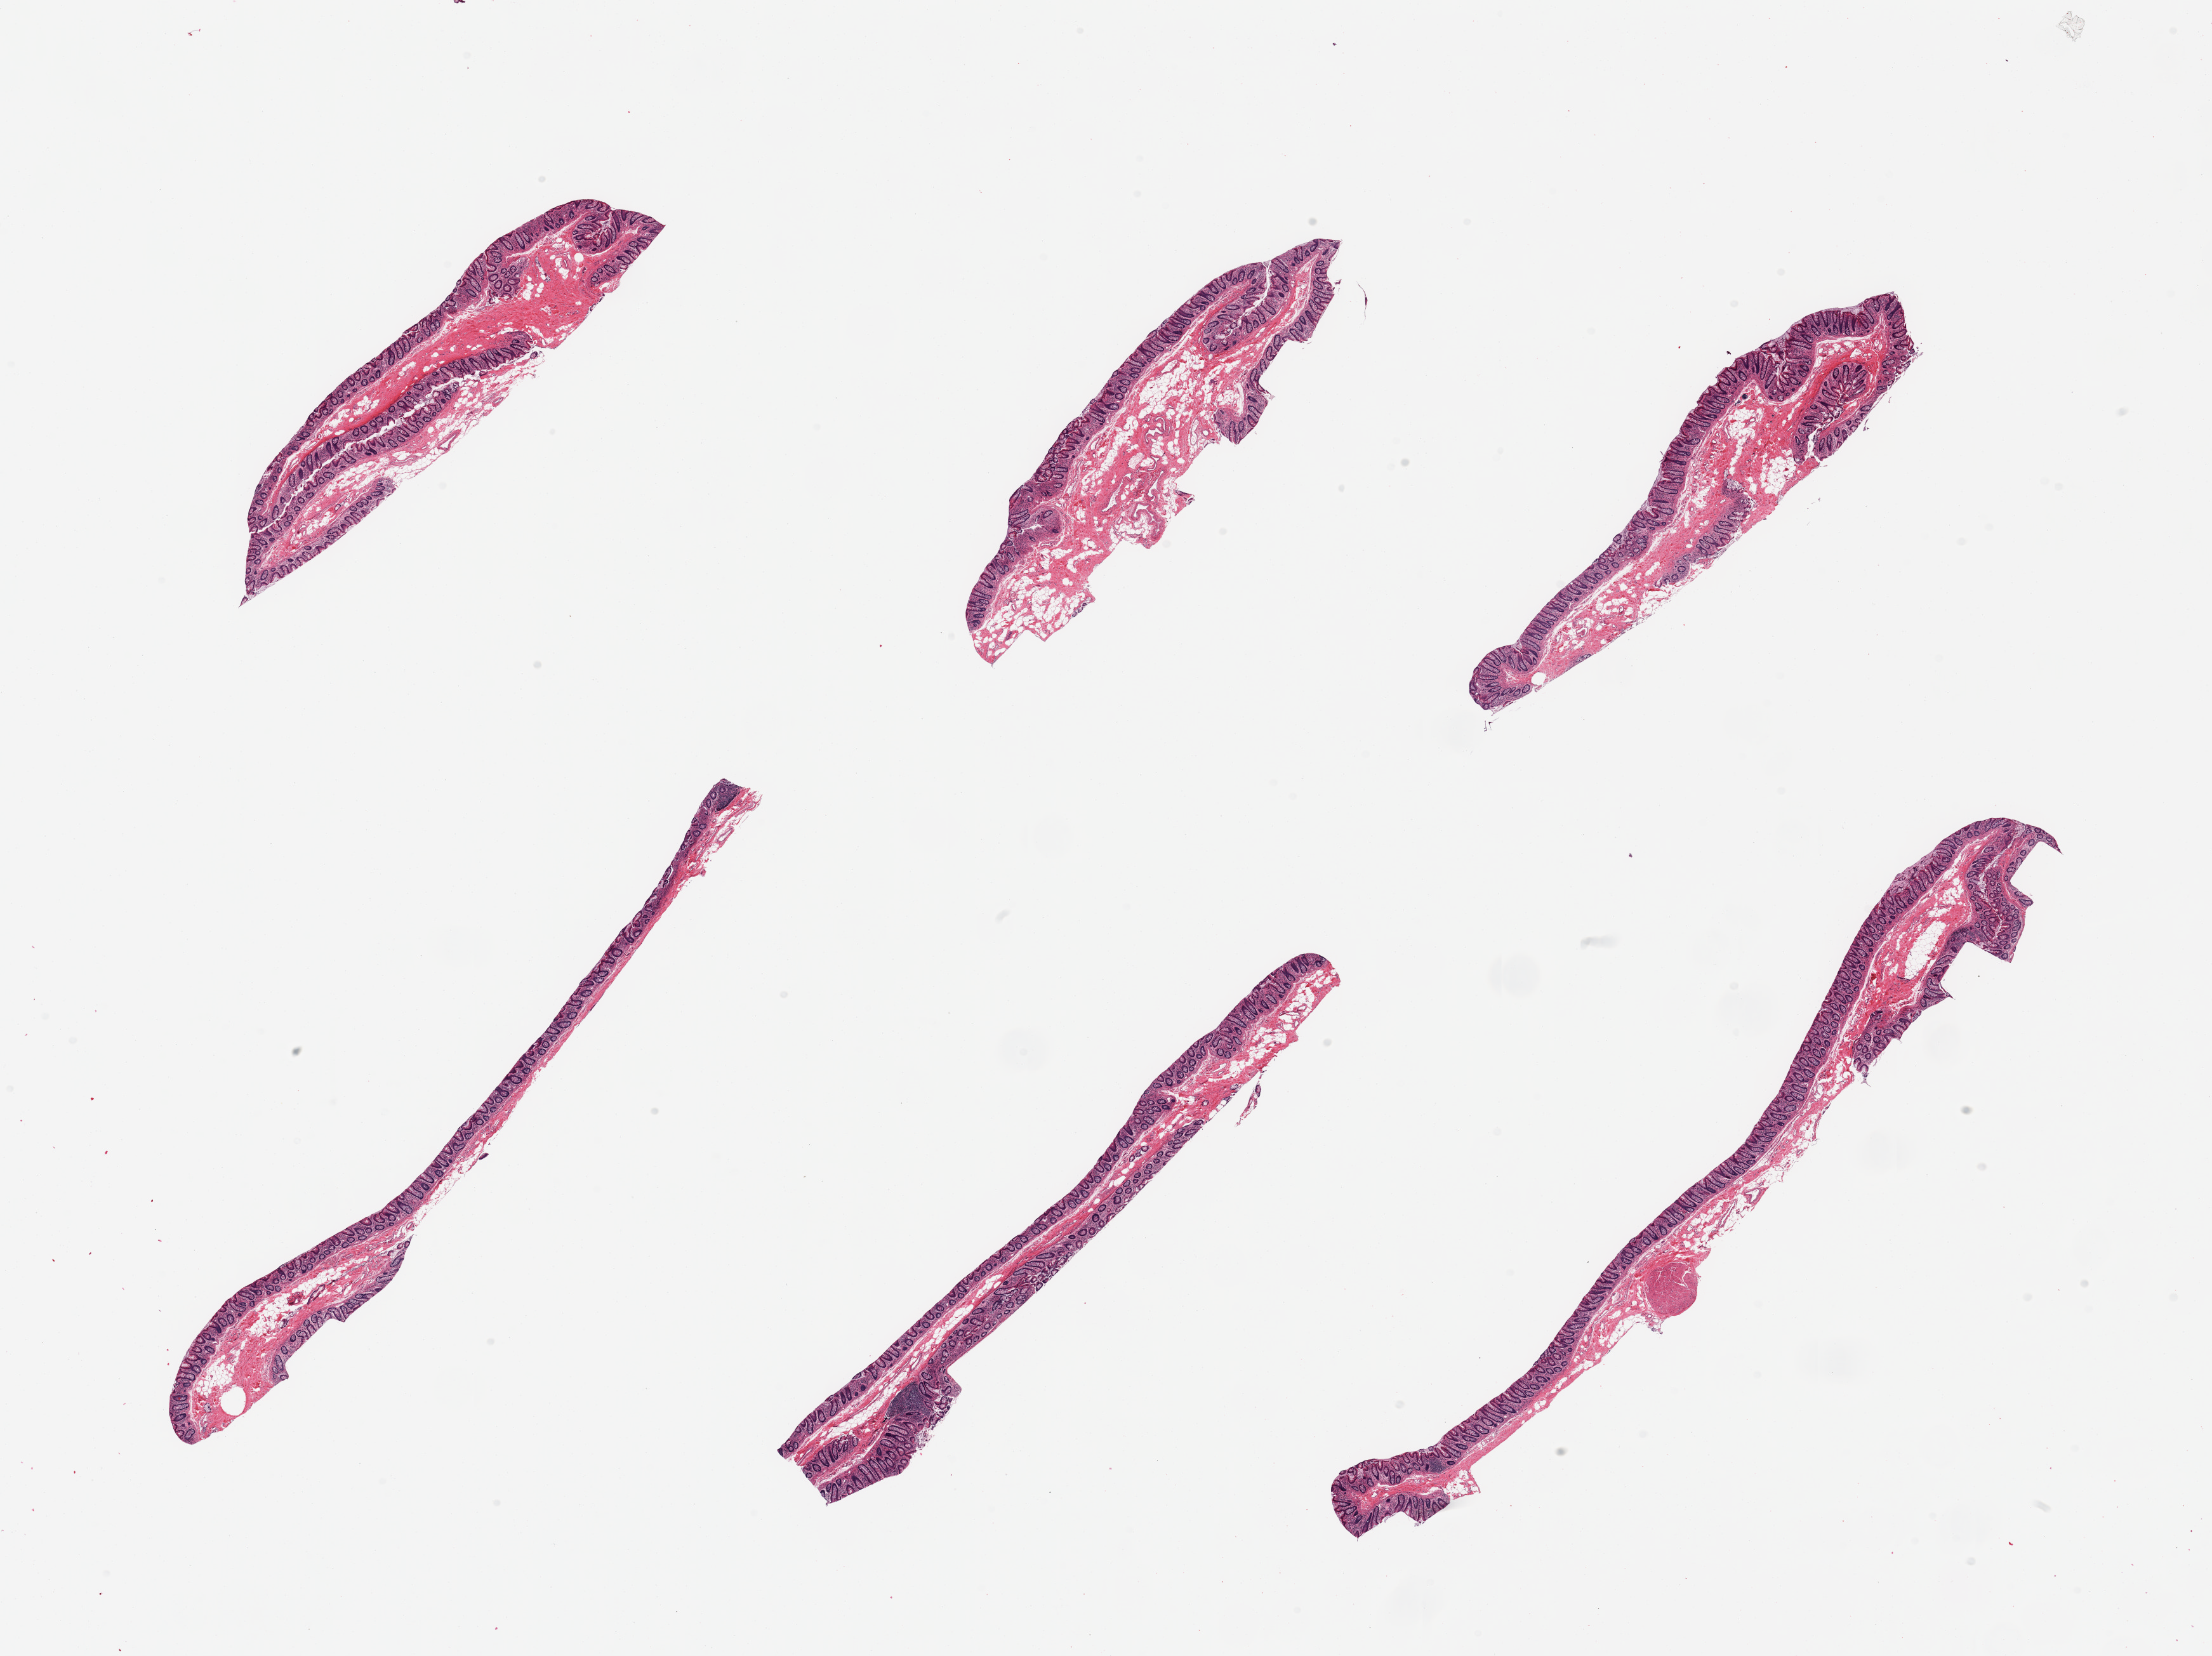
Whole-slide image, H&E stain — a low-resolution overview of the entire scanned area, about 27.6 x 20.6 mm (slide scanned at 20x). PAXgene-fixed paraffin-embedded (PFPE) section. Target tissue: transverse colon. Donor tissue sample.
Pathologist's review note for this sample: 6 pieces, well- preserved mucosa up to ~0.35mm, ~20-50% of thickness.